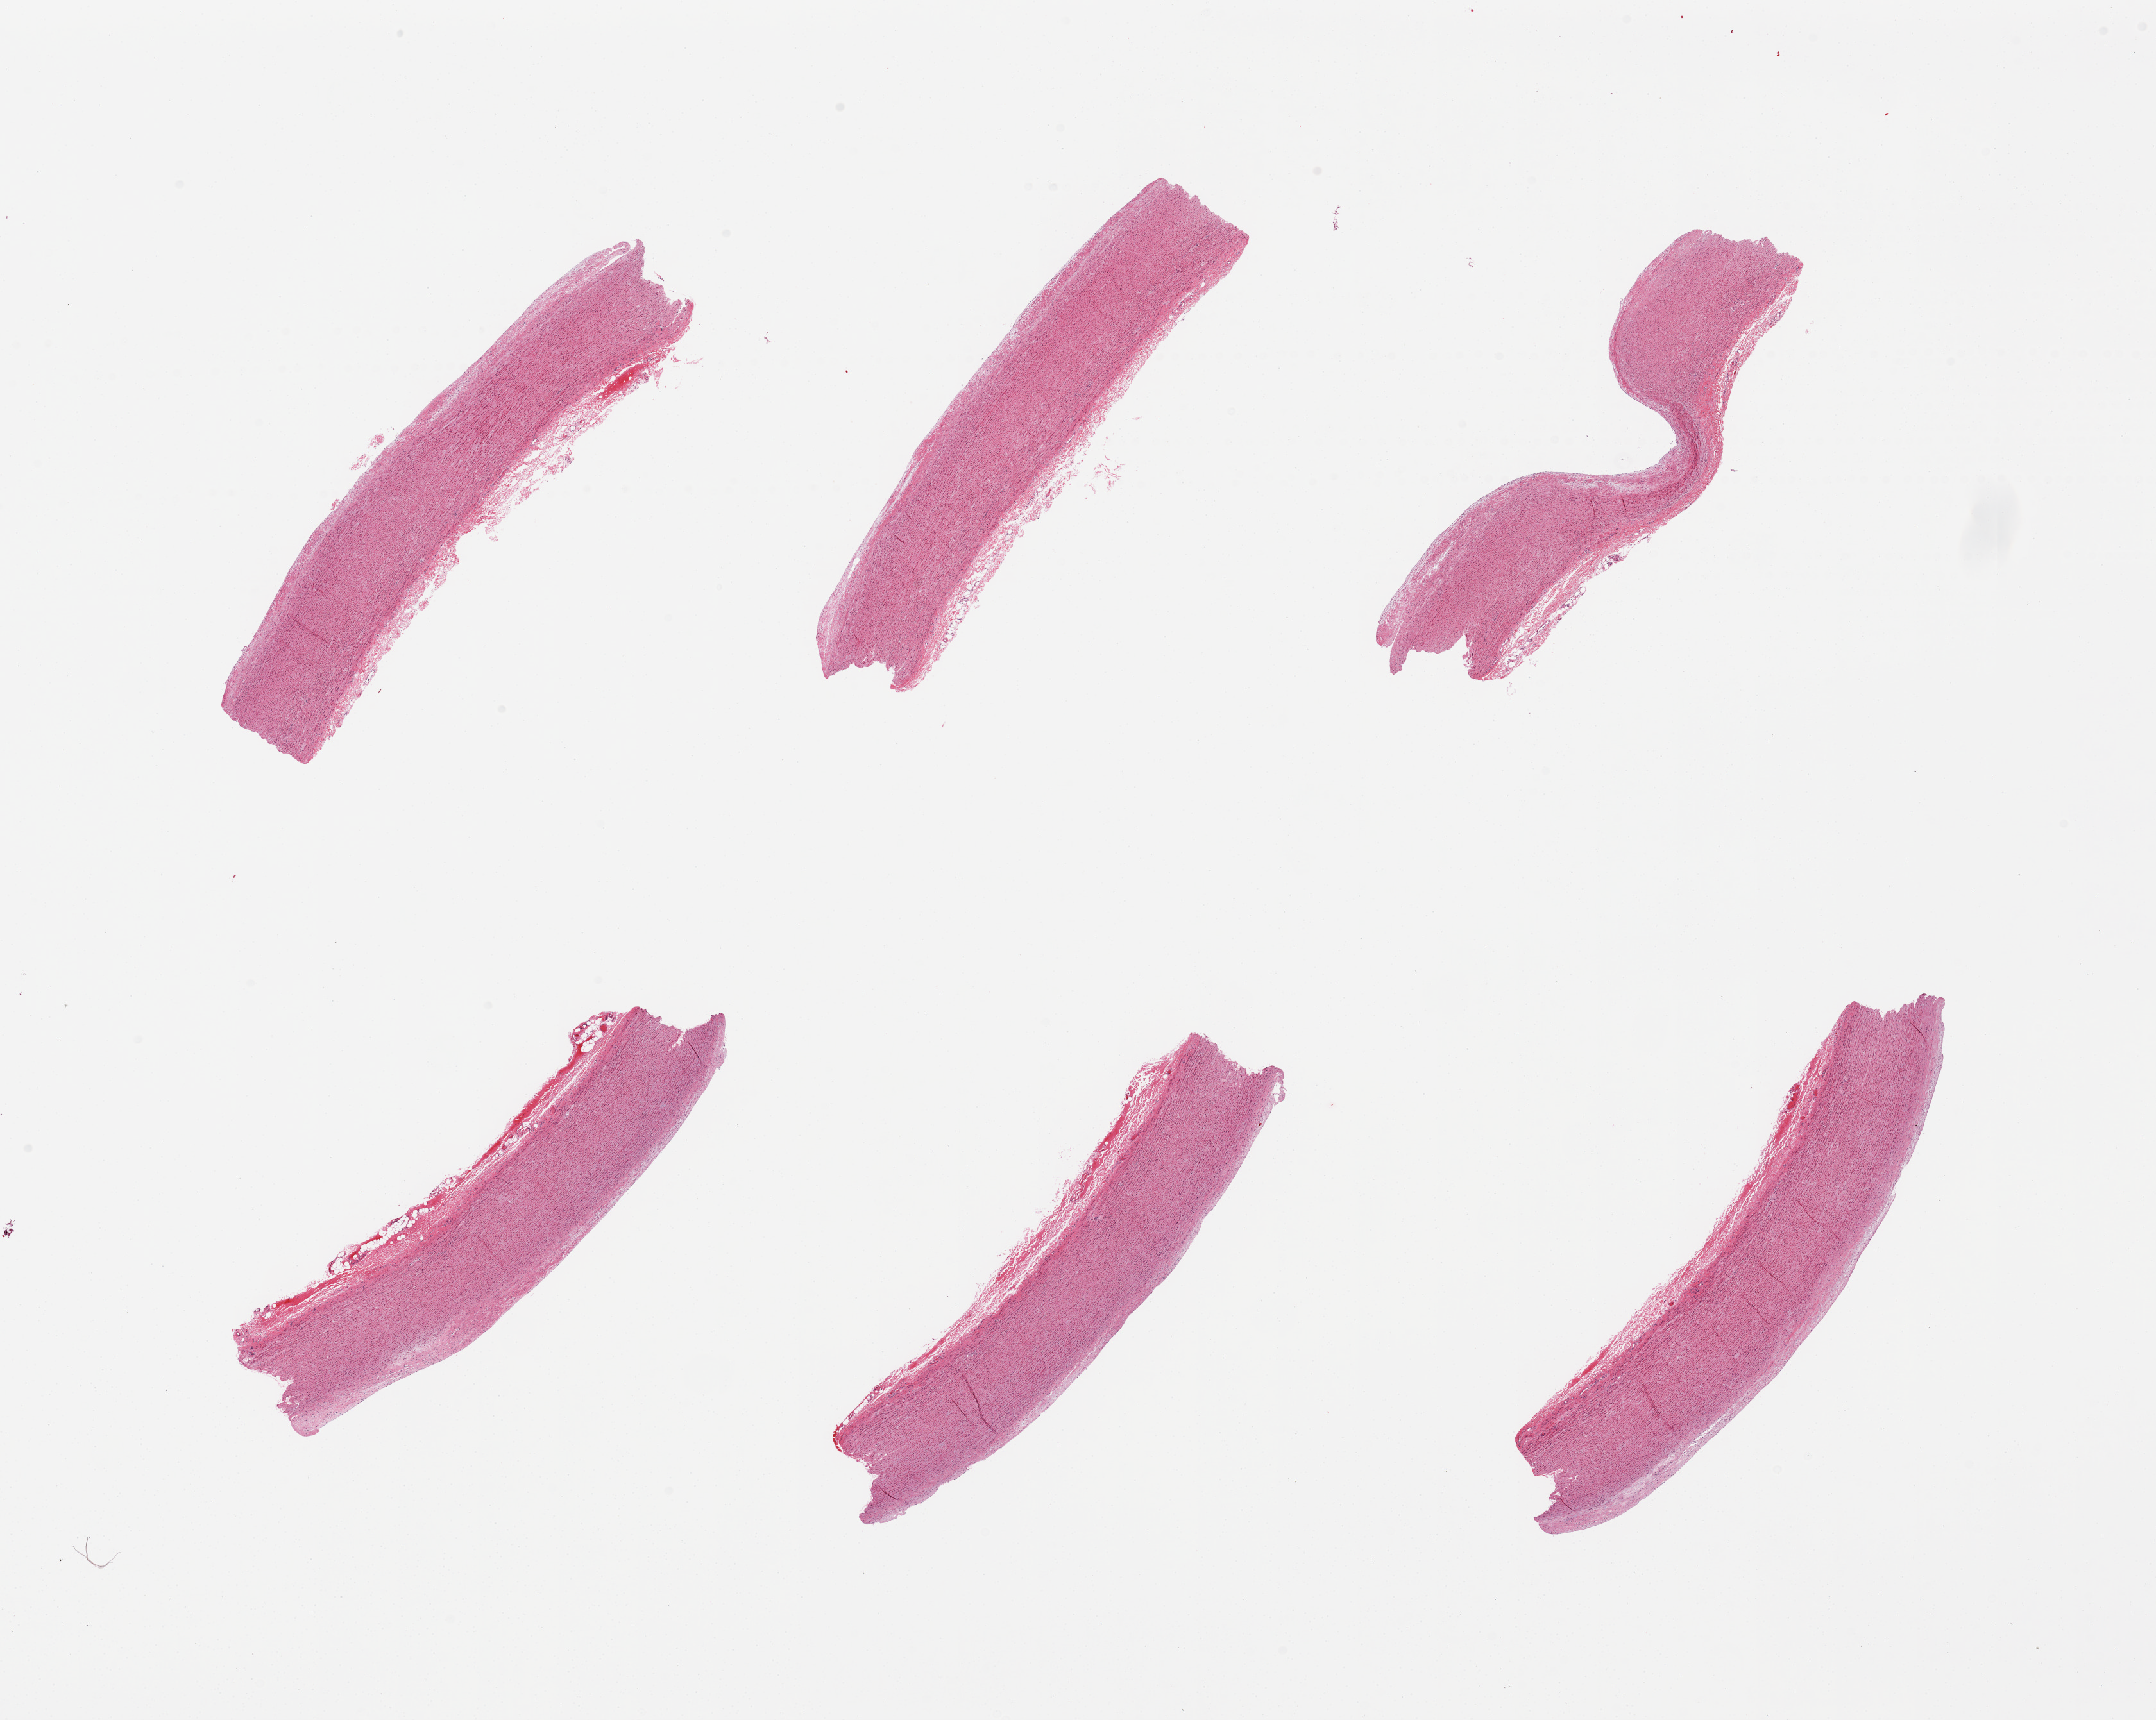
H&E whole-slide image — whole scanned area (about 26.6 x 21.2 mm, acquisition: 20x scan) shown as a low-resolution overview, PAXgene-fixed paraffin-embedded (PFPE) section, target tissue: aorta, tissue donor sample. Male donor.
Reviewer comment on this tissue sample: 6 pieces, adherenet serosa on several up to ~0.4mm; Minimal atherosis, <0.1mm.